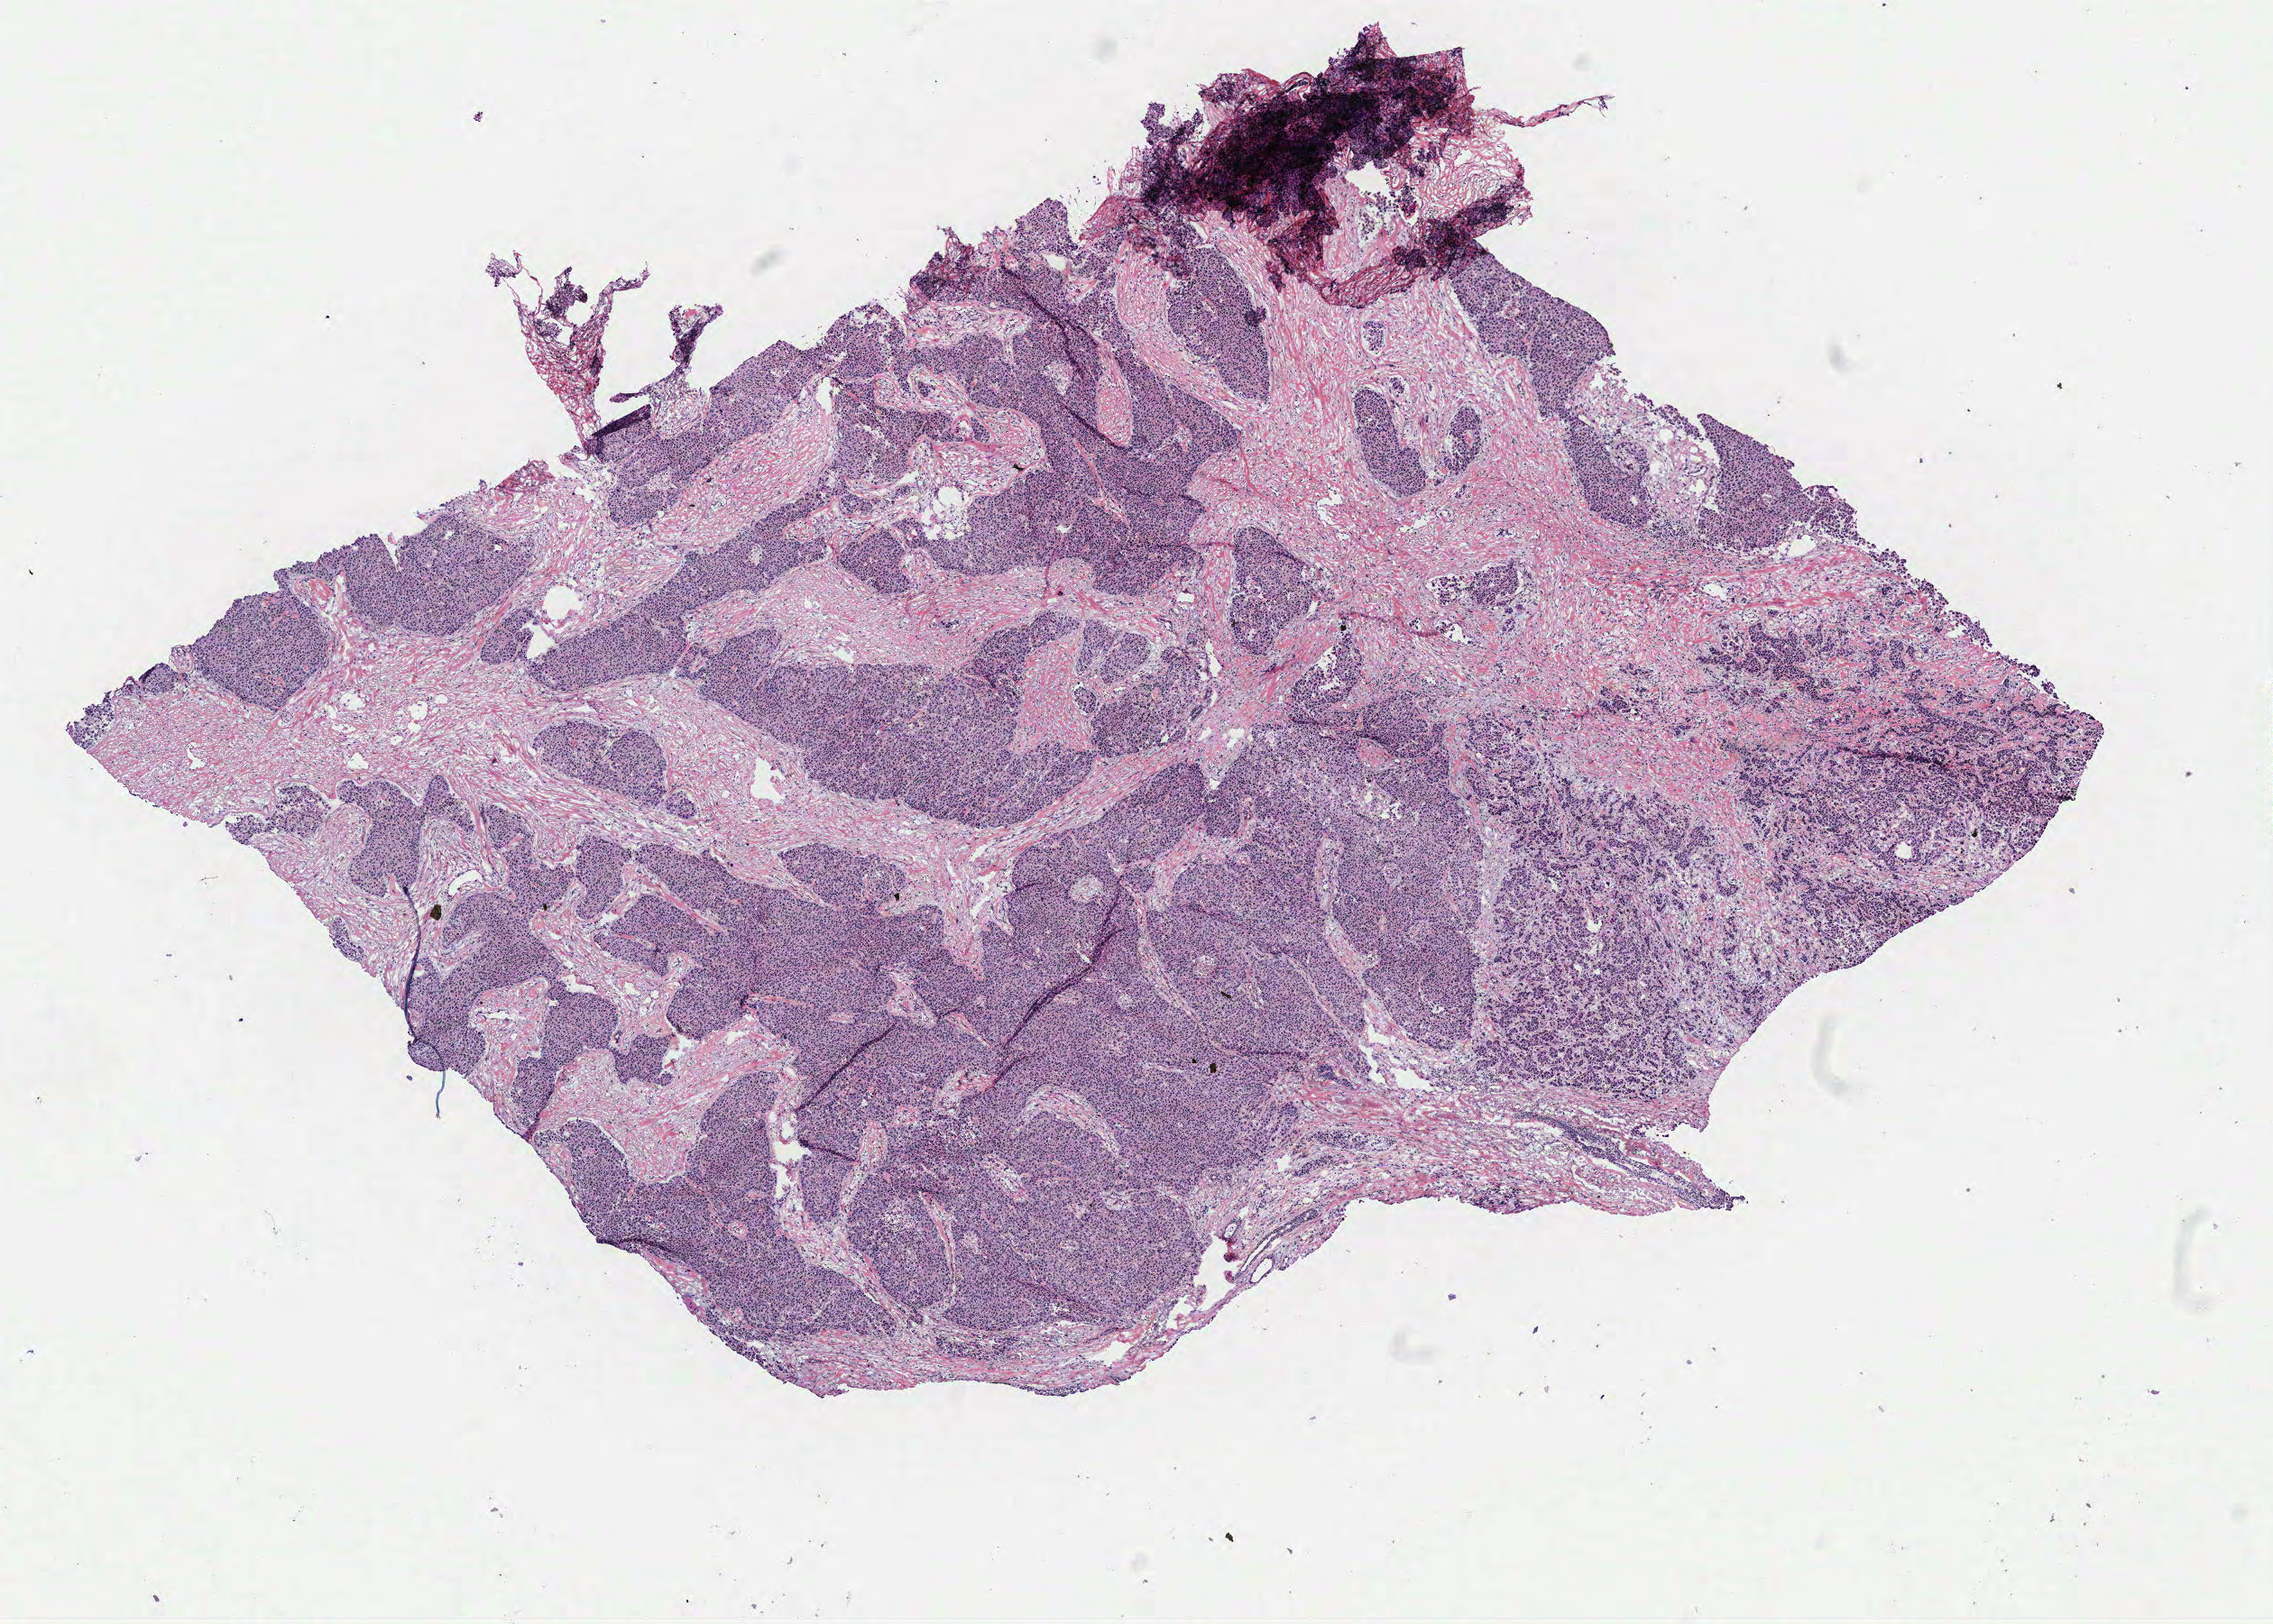
Whole-slide histology image, Hematoxylin and eosin (H&E) stained — shown as a low-resolution overview of the whole scanned area (about 10.1 x 7.2 mm); breast, tumour tissue. Female, 78 y/o.
- AJCC pathologic stage: IIB
- histologic diagnosis: Infiltrating duct carcinoma, NOS